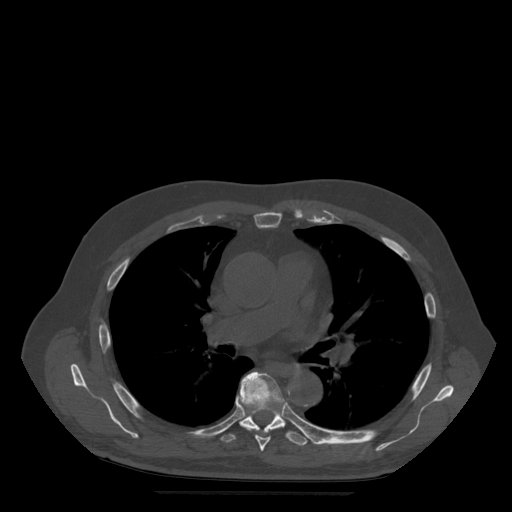
CT including the spine, one axial slice; slice 344 of 522 in the series (ordered by position); bone window (W 1800 / L 400 HU); 1.25 mm slice thickness; 512 × 512 image matrix. Patient age 72 years. From the clinical record (not read from this slice): primary cancer: prostate.
Structures marked on this image (semi-automatic segmentation, software-assisted and operator-edited):
- T6 vertebra: bounding box (x1, y1, x2, y2) in pixels: (236, 372, 285, 452)
- T7 vertebra: (220, 411, 309, 446)